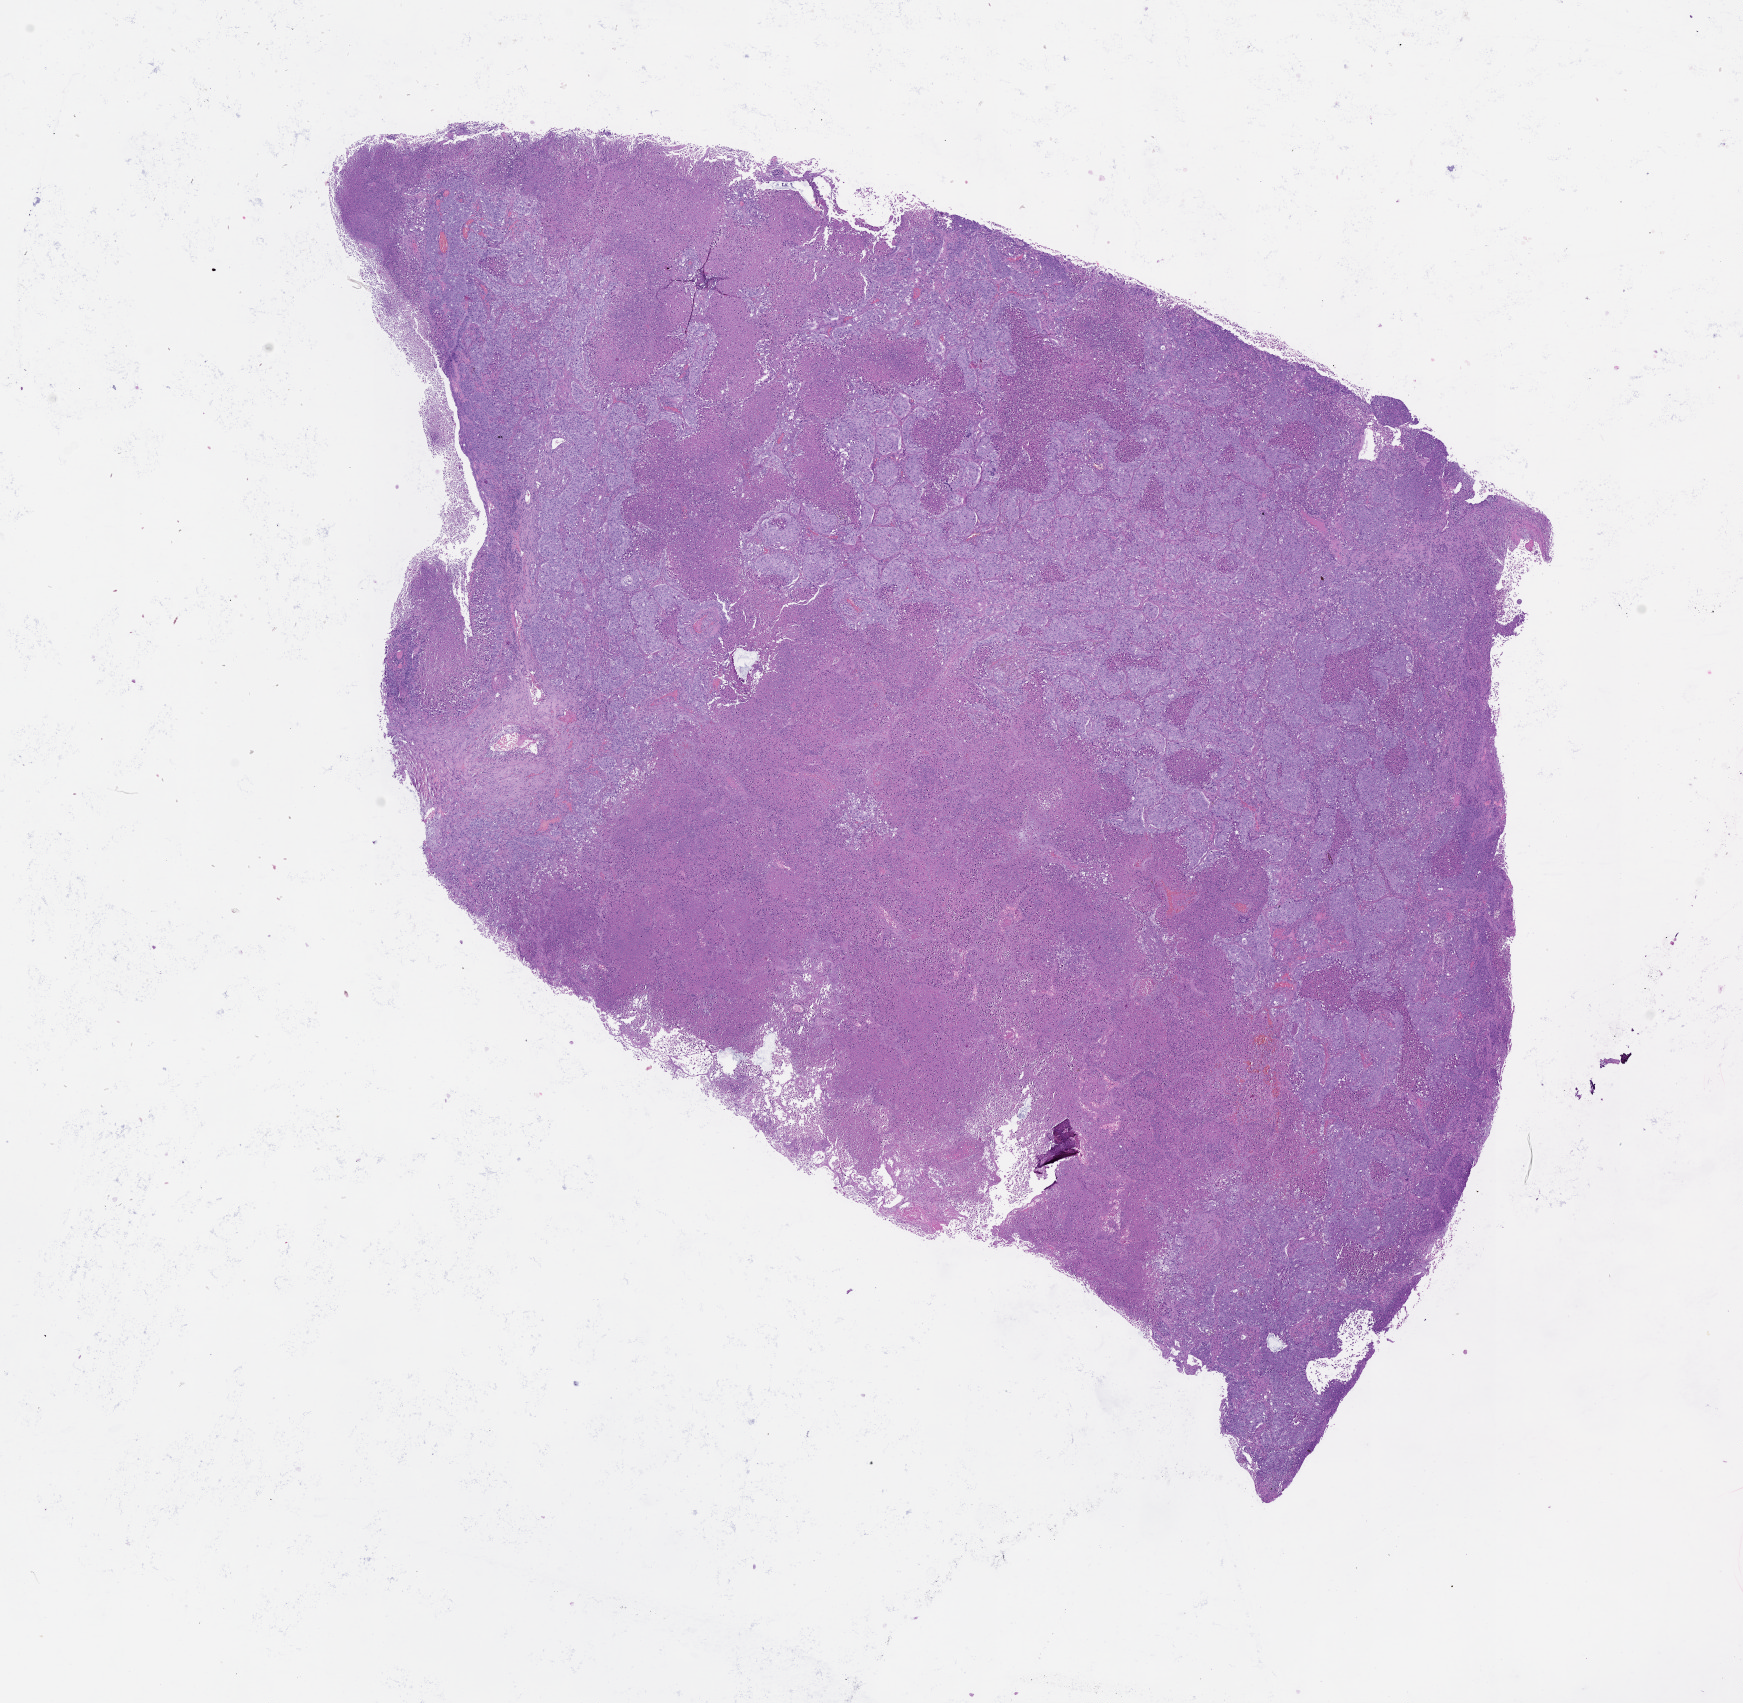
Hematoxylin and eosin (H&E) stained whole-slide image, whole scanned area (about 14.0 x 13.7 mm, slide scanned at 20x) shown as a low-resolution overview; lung, tumour tissue. Male, 67 y/o.
Patient diagnosis (cohort enrolment): squamous cell carcinoma (lung).